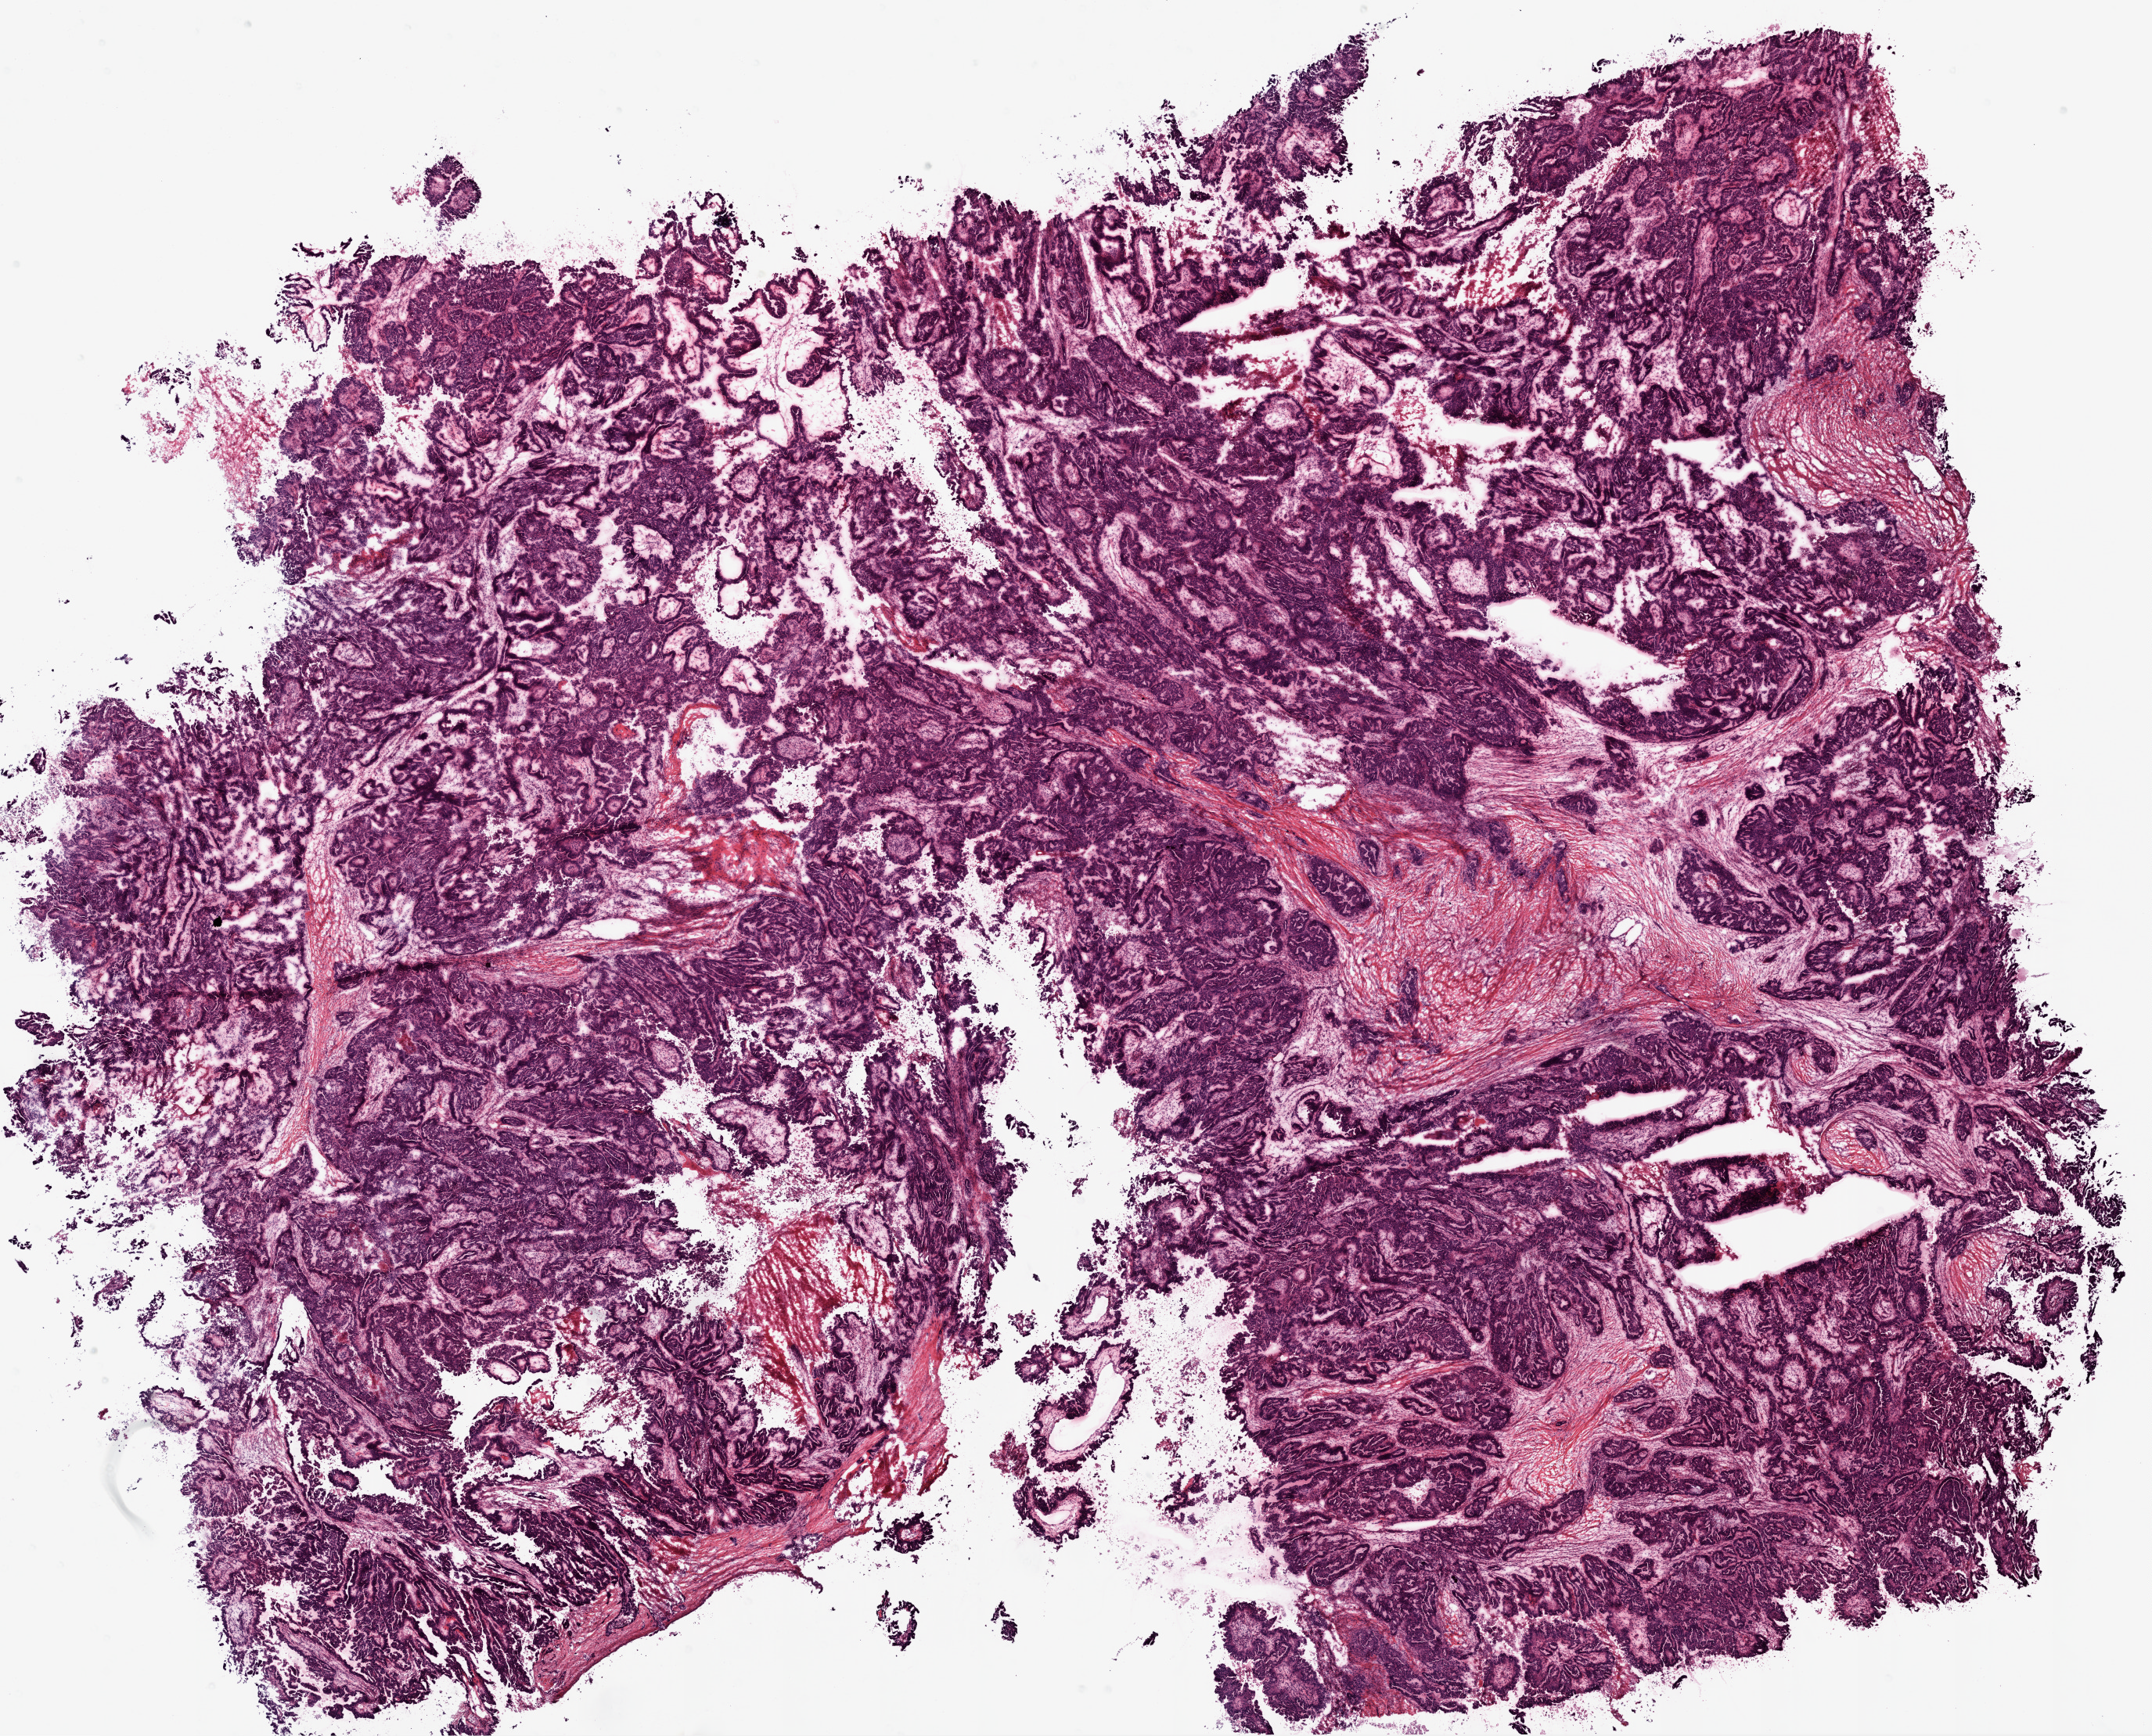
Whole-slide histology image, H&E-stained — whole scanned area (about 22.1 x 17.8 mm, from a 20x scan) shown as a low-resolution overview, frozen section, ovary, primary tumour sample. Patient: female, age at initial diagnosis 52 years. Pathologist review of this section (percent, as recorded): tumour cells 90%, tumour nuclei 95%.
Pathologic diagnosis: Serous cystadenocarcinoma, NOS.